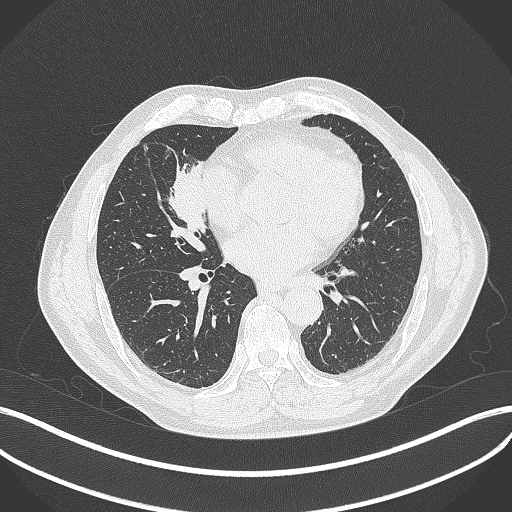
Chest CT, one axial slice; position 177 of 429 along the scan axis; 120 kVp; lung window (W 1500 / L -600 HU); 1 mm slice thickness; 512 × 512 image matrix. Male patient, age 61 years. Case-level facts recorded for this patient, not image findings: clinical TNM (as recorded): T2b N1 M0.
Outlined on this slice (rectangle marked by the reading radiologist):
- lung tumour (recorded histology: squamous cell carcinoma): bounding box (x1, y1, x2, y2) in pixels: (165, 158, 212, 241)